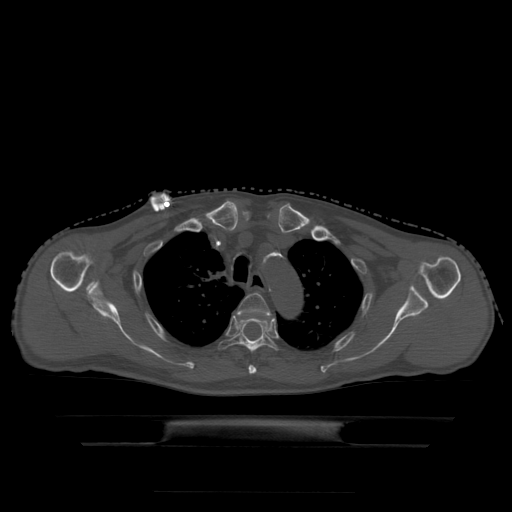
CT including the spine, one axial slice. Position 360 of 522 along the scan axis. Bone window (W 1800 / L 400 HU). 1.25 mm slice thickness. 512 × 512 image matrix, field of view 436 × 436 mm. Patient age 68 years. Case-level facts recorded for this patient, not image findings: primary cancer: urothelial.
Annotated regions visible in this slice (semi-automatically segmented with operator editing):
- T3 vertebra: bounding box <237,293,271,375> (left, top, right, bottom; pixels)
- T4 vertebra: <218,315,278,353>